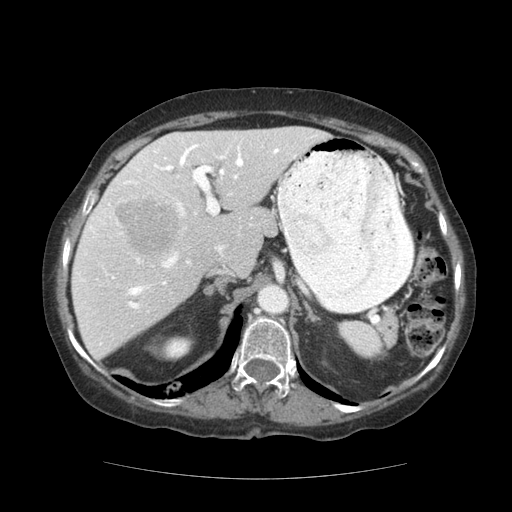
Contrast-enhanced abdominal CT (liver protocol), one axial slice; slice 78 of 111 in the series (ordered by position); reconstruction kernel STANDARD; 140 kVp; soft-tissue window (W 400 / L 40 HU); 512 × 512 image matrix, field of view 360 × 360 mm. Case-level facts recorded for this patient, not image findings: diagnosis: hepatocellular carcinoma (patient treated with transarterial chemoembolisation; whether this scan precedes or follows treatment is not stated here); TNM stage (as recorded): Stage-I; Child-Pugh class: A.
Annotated regions visible in this slice (semi-automatic segmentation, software-assisted and operator-edited):
- liver parenchyma outside the tumour (the mass and vessels are separate outlines, so this box may not span the whole liver): bounding box <72,126,329,358> (left, top, right, bottom; pixels)
- mass: <116,197,178,256>
- liver vessels: <77,135,315,345>